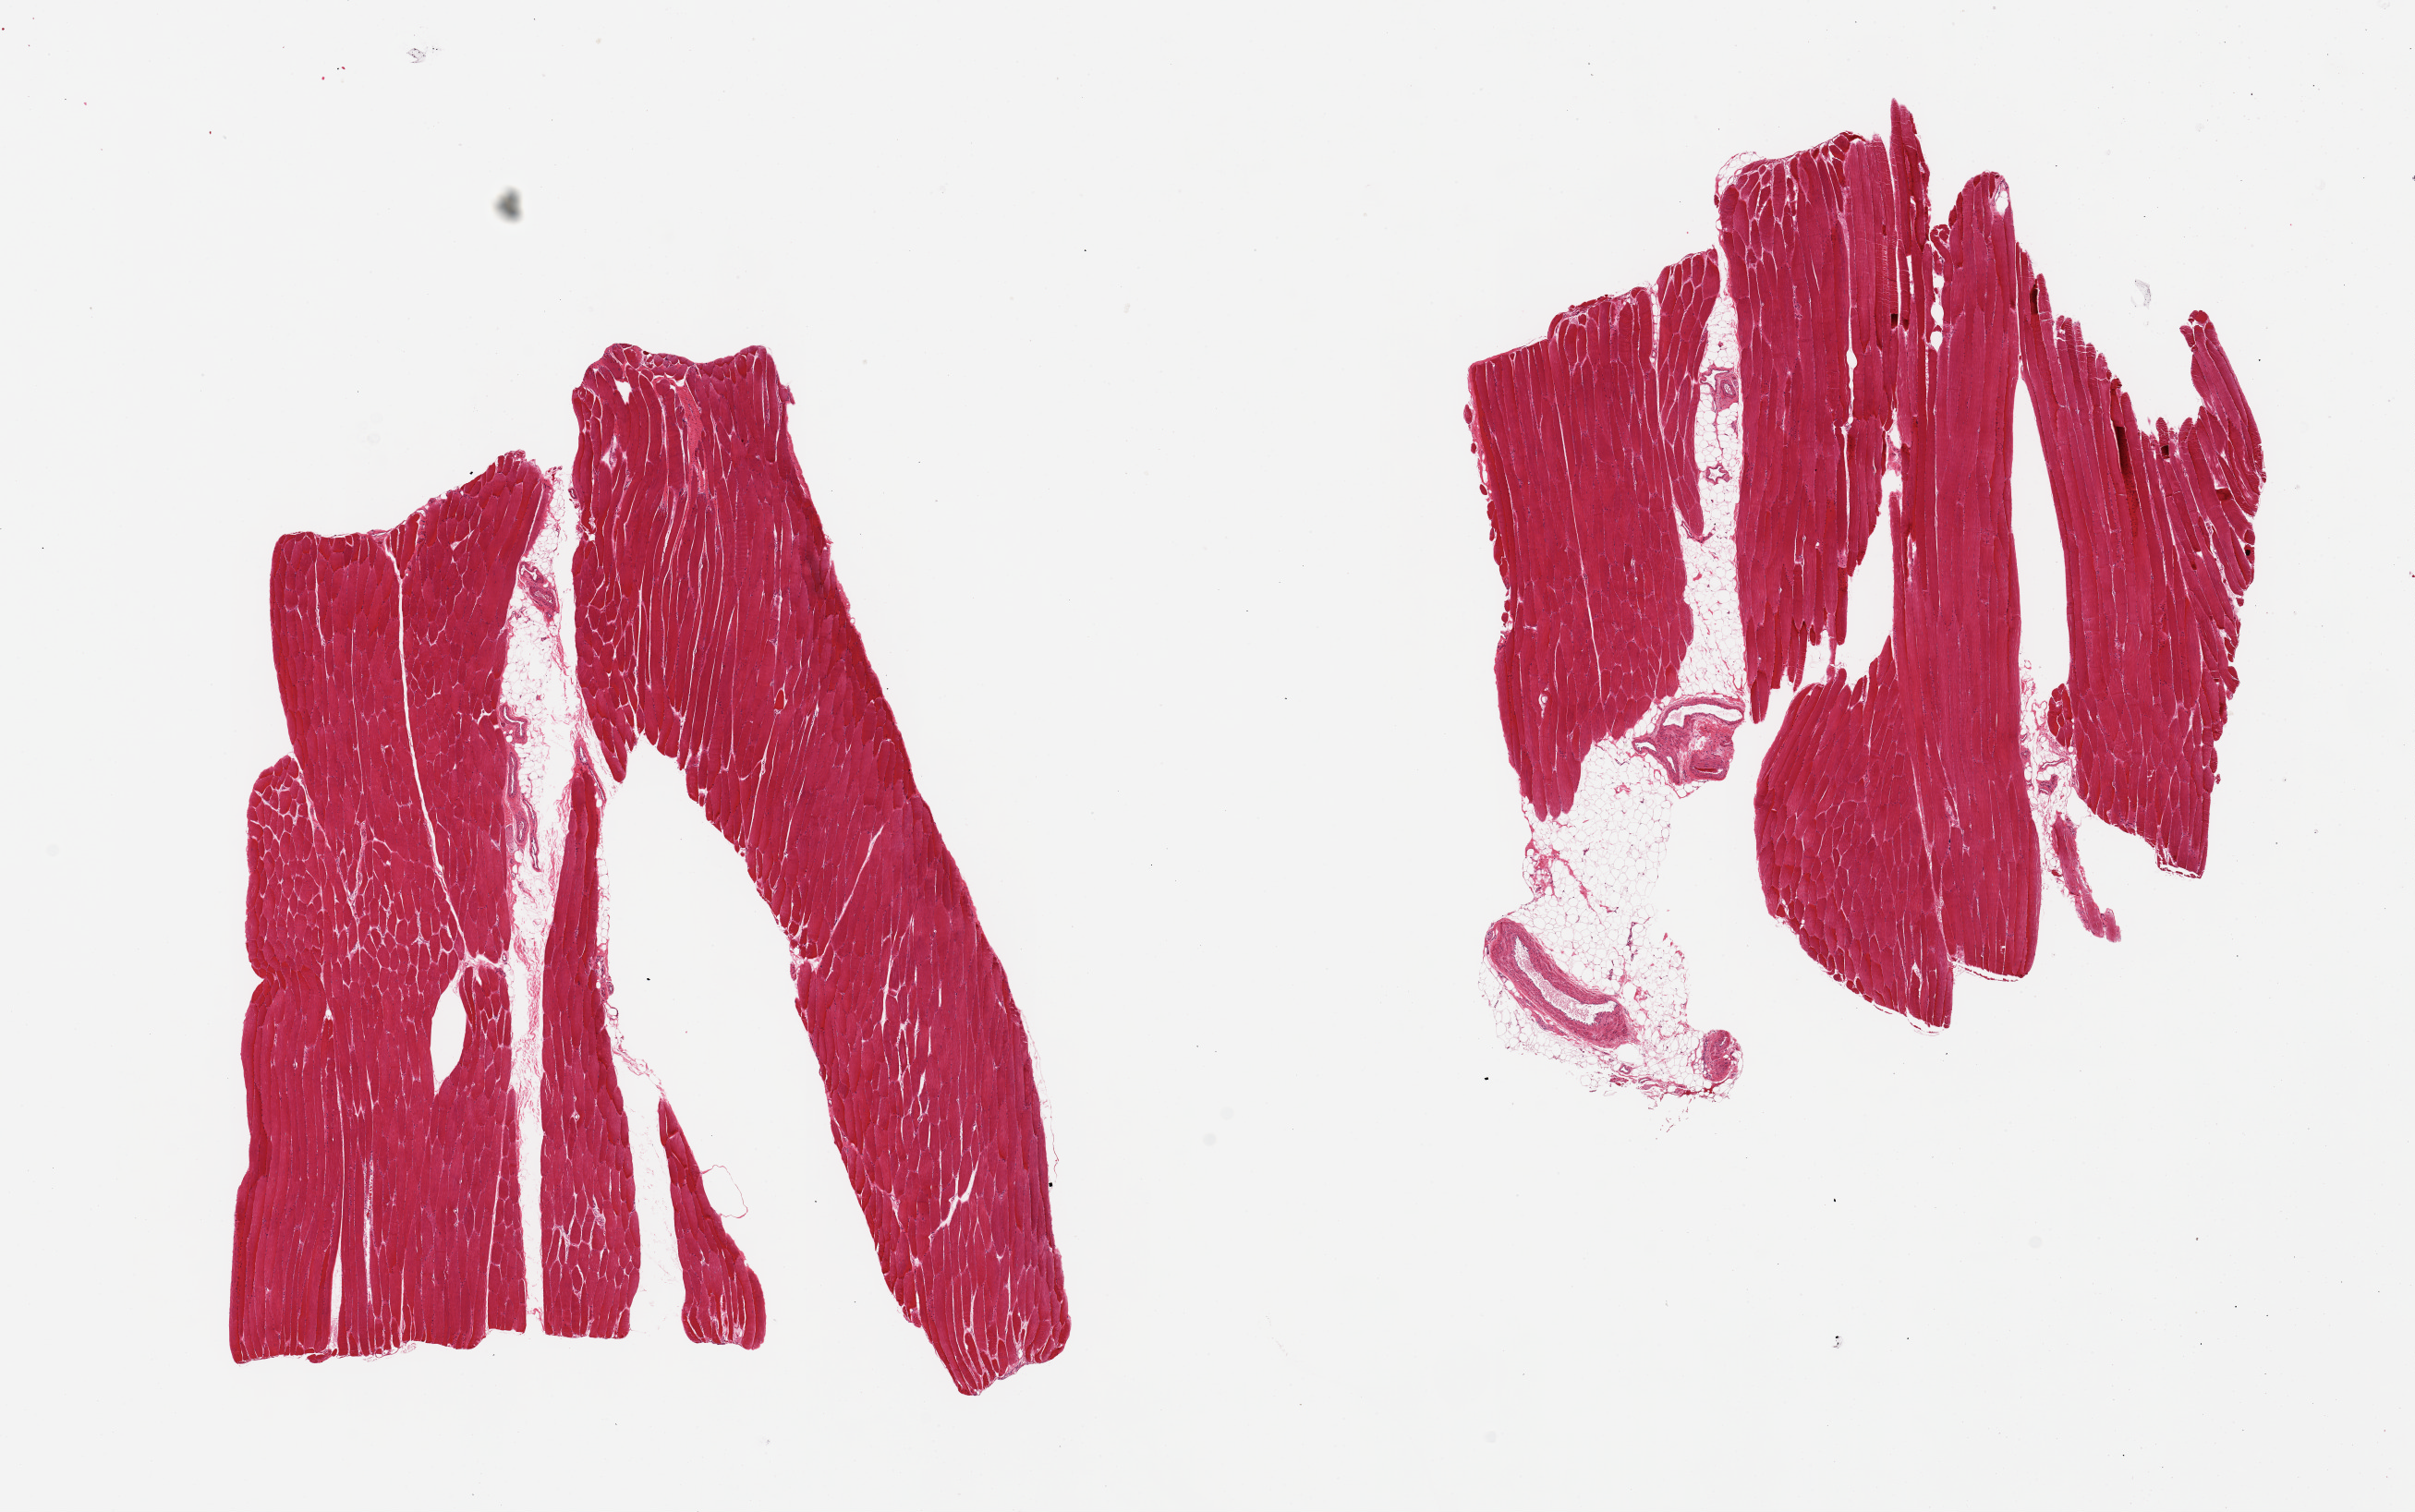
Whole-slide image, hematoxylin and eosin (H&E) stain — low-resolution overview of the scanned area, about 20.7 x 12.9 mm (acquisition: 20x scan). PAXgene-fixed paraffin-embedded (PFPE) section. Section of skeletal muscle (target tissue). Tissue donor sample. Donor sex: male.
* pathologist's review note for this sample: 2 pieces; 10% internal fat